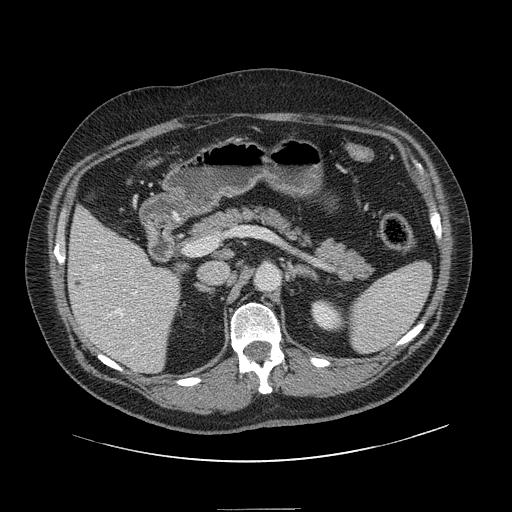
Contrast-enhanced abdominal CT, one axial slice; position 74 of 154 along the scan axis; intravenous contrast given; soft-tissue window (W 400 / L 40 HU); 512 × 512 image matrix. Male patient, age 61 years. Case-level facts recorded for this patient, not image findings: diagnosis: colorectal cancer liver metastases, imaged before liver resection; multiple liver metastases: yes; largest metastasis: 2.6 cm; disease in both lobes: yes.
Outlined on this slice (manually delineated by an expert):
- hepatic veins: bounding box [x1, y1, x2, y2] px = [92, 265, 137, 351]
- liver: [69, 210, 180, 372]
- planned liver remnant (the part of the liver to remain after resection): [70, 210, 180, 365]
- portal vein (with intrahepatic branches): [131, 273, 134, 322]
- liver metastasis: [73, 278, 83, 289]